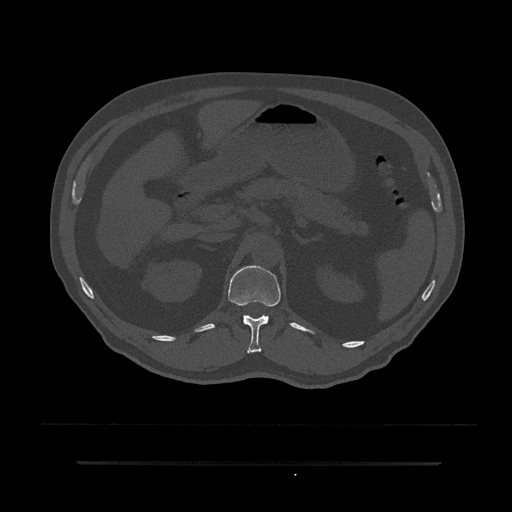
CT including the spine, one axial slice; position 196 of 797 along the scan axis; bone window (W 1800 / L 400 HU); 512 × 512 image matrix, field of view 464 × 464 mm. Patient: male, 59 years. Case-level facts recorded for this patient, not image findings: primary cancer: bile ducts; vertebrae with lytic lesions (as recorded): T10.
Annotated regions visible in this slice (semi-automatic segmentation, software-assisted and operator-edited):
- T12 vertebra: bounding box (x1, y1, x2, y2) in pixels: (228, 265, 281, 353)